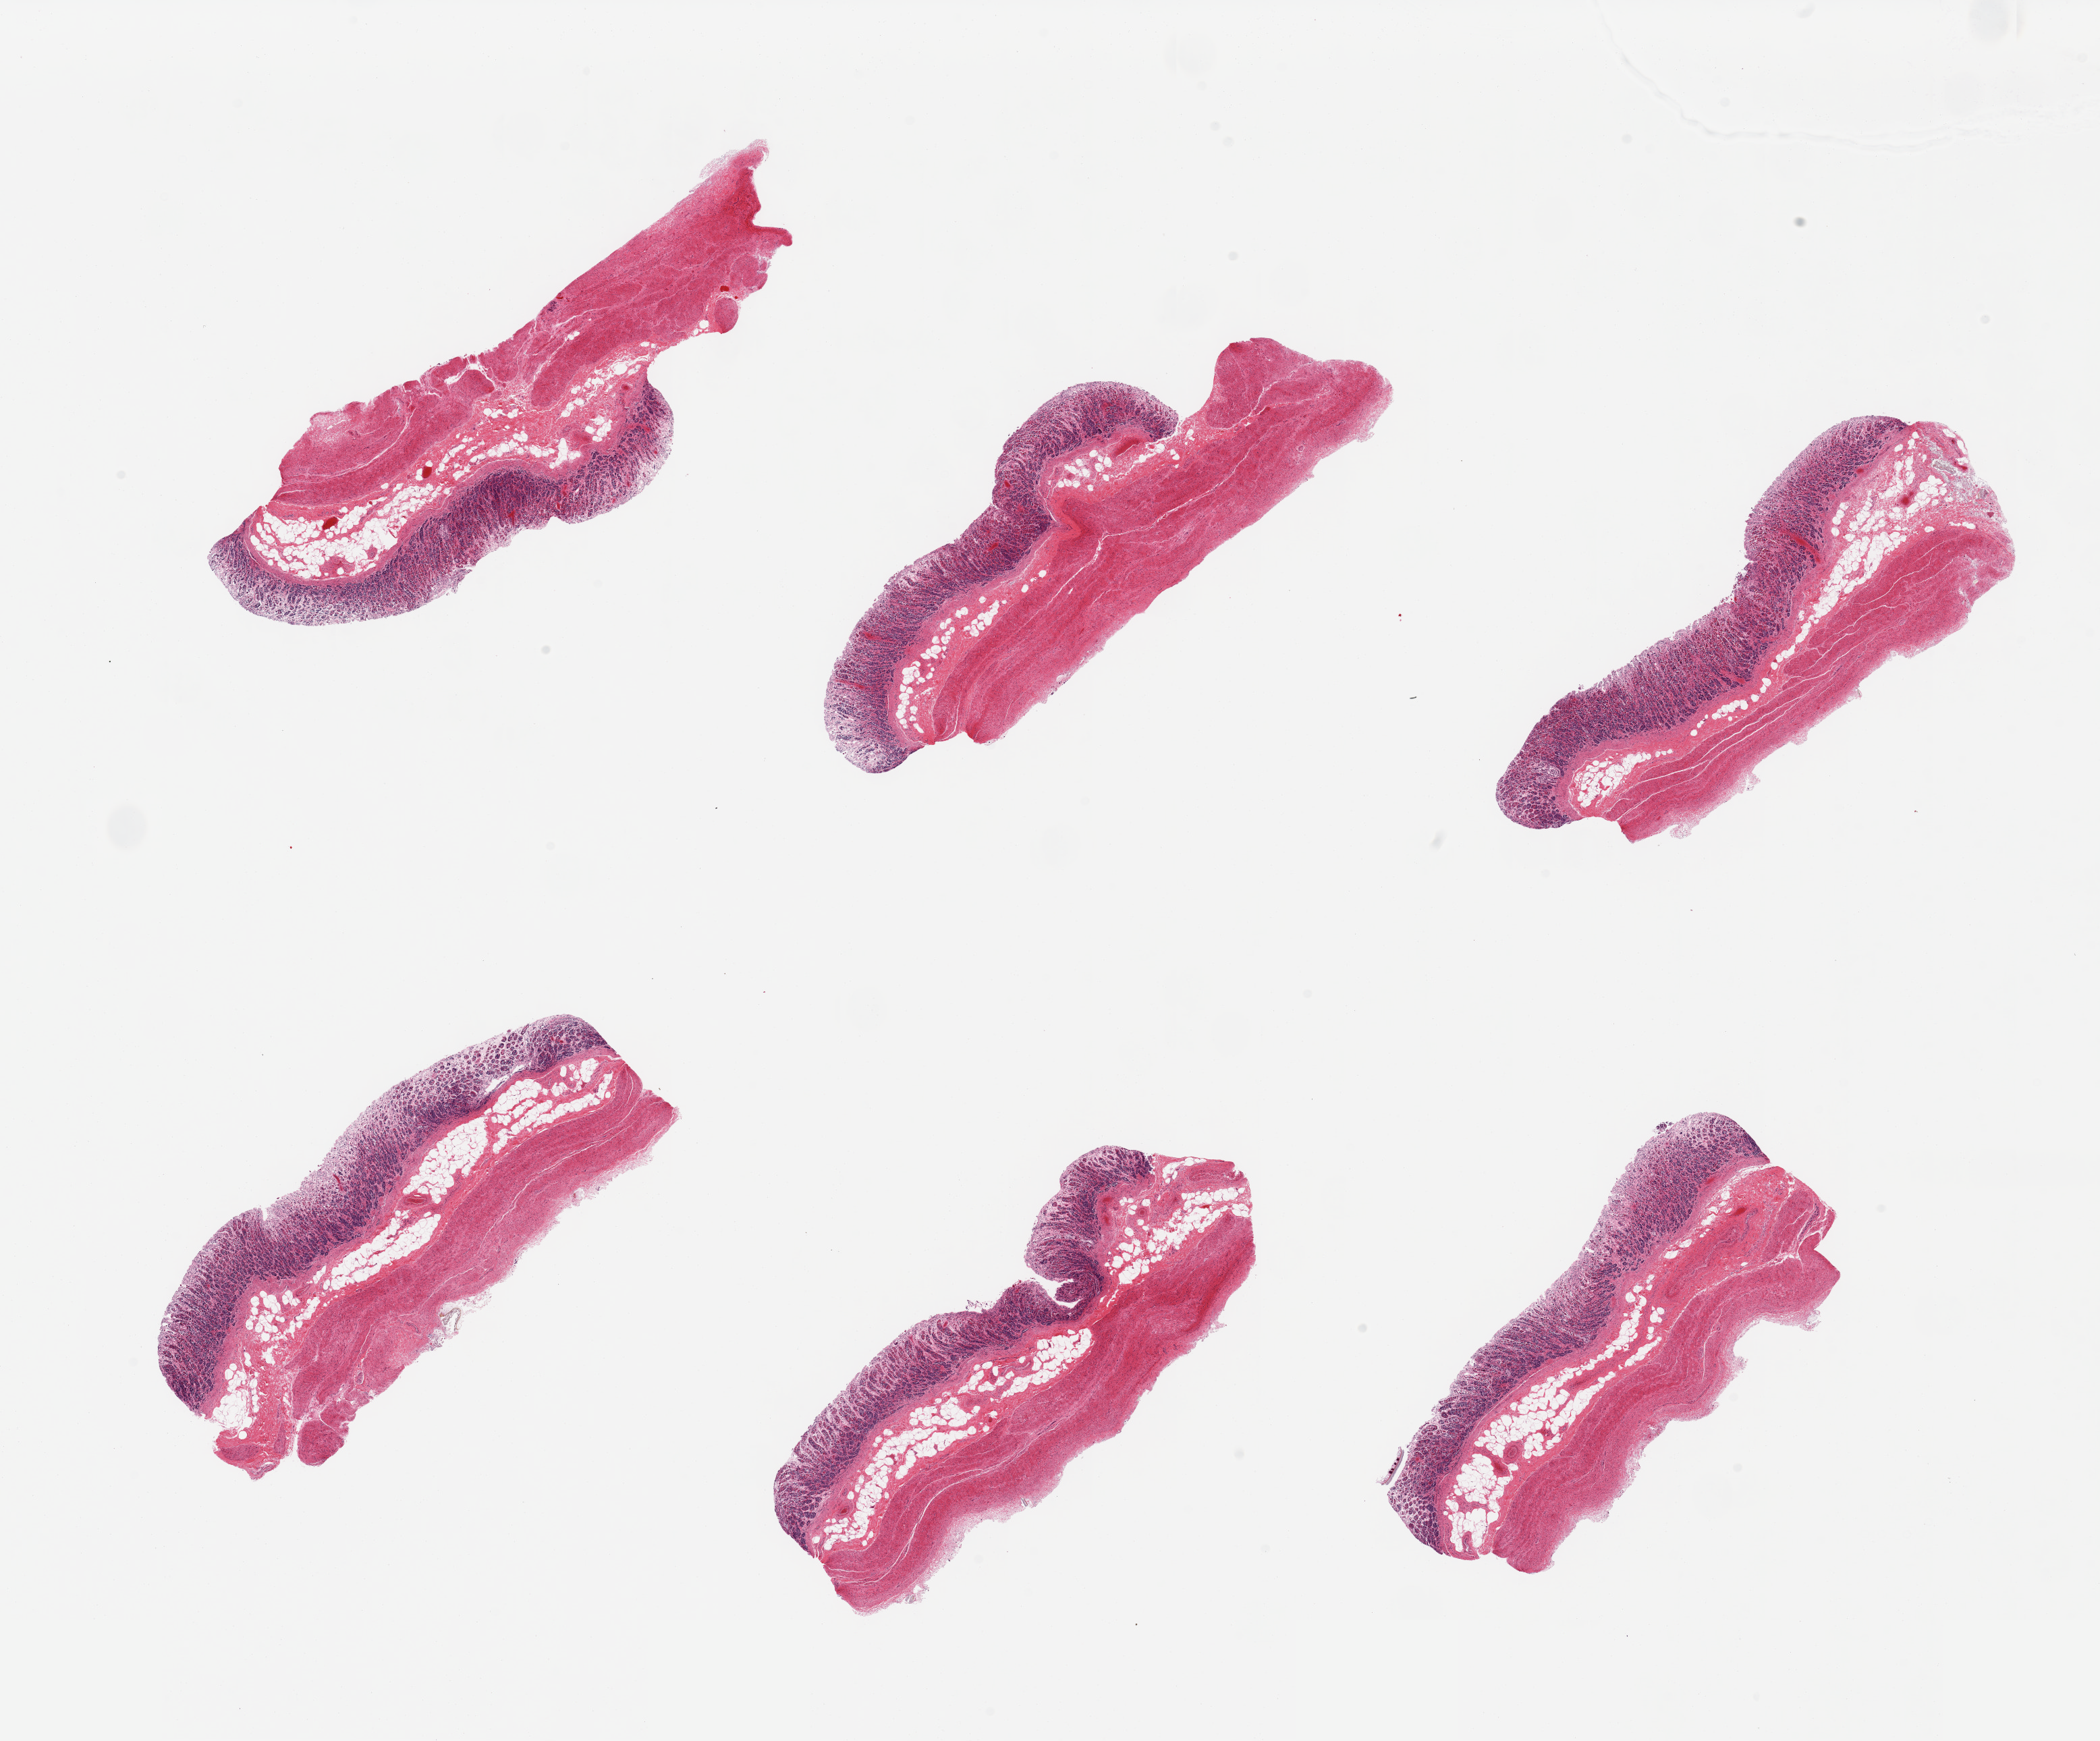
Whole-slide image, H&E stain, low-resolution overview of the scanned area, about 24.6 x 20.4 mm (from a 20x scan), PAXgene-fixed, paraffin-embedded tissue, target tissue: stomach, donor tissue sample. Donor sex: male.
- reviewer comment on this tissue sample: 6 pieces; superficial mucosa autolyzed; vegetable material on serosal surface